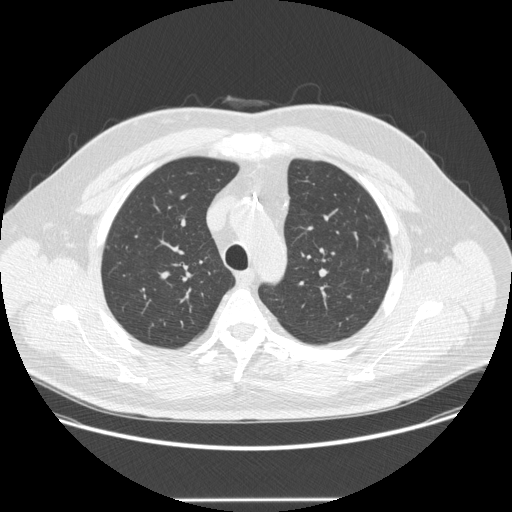
Axial slice from a low-dose chest CT screening exam; baseline annual screen; lung window (W 1500 / L -600 HU); 1.25 mm slice thickness; 120 kVp; slice 61 of 252 in the series; 512 × 512 image matrix. Male, age 55 years at enrolment. Former smoker at enrolment.
• Lesion marked by an expert reader, bounding box (x1, y1, x2, y2) in pixels: (373, 234, 403, 265).
• Screening reader's record for this exam (one nodule recorded; not confirmed to be the boxed lesion): non-calcified nodule or mass ≥4 mm, left upper lobe, 5 × 4 mm, smooth margins, soft tissue attenuation.
• Later outcome: lung cancer diagnosed 462 days after this screen — adenocarcinoma, NOS, left upper lobe, moderately differentiated (G2), stage IA (AJCC 6th edition), 9 mm at pathology.